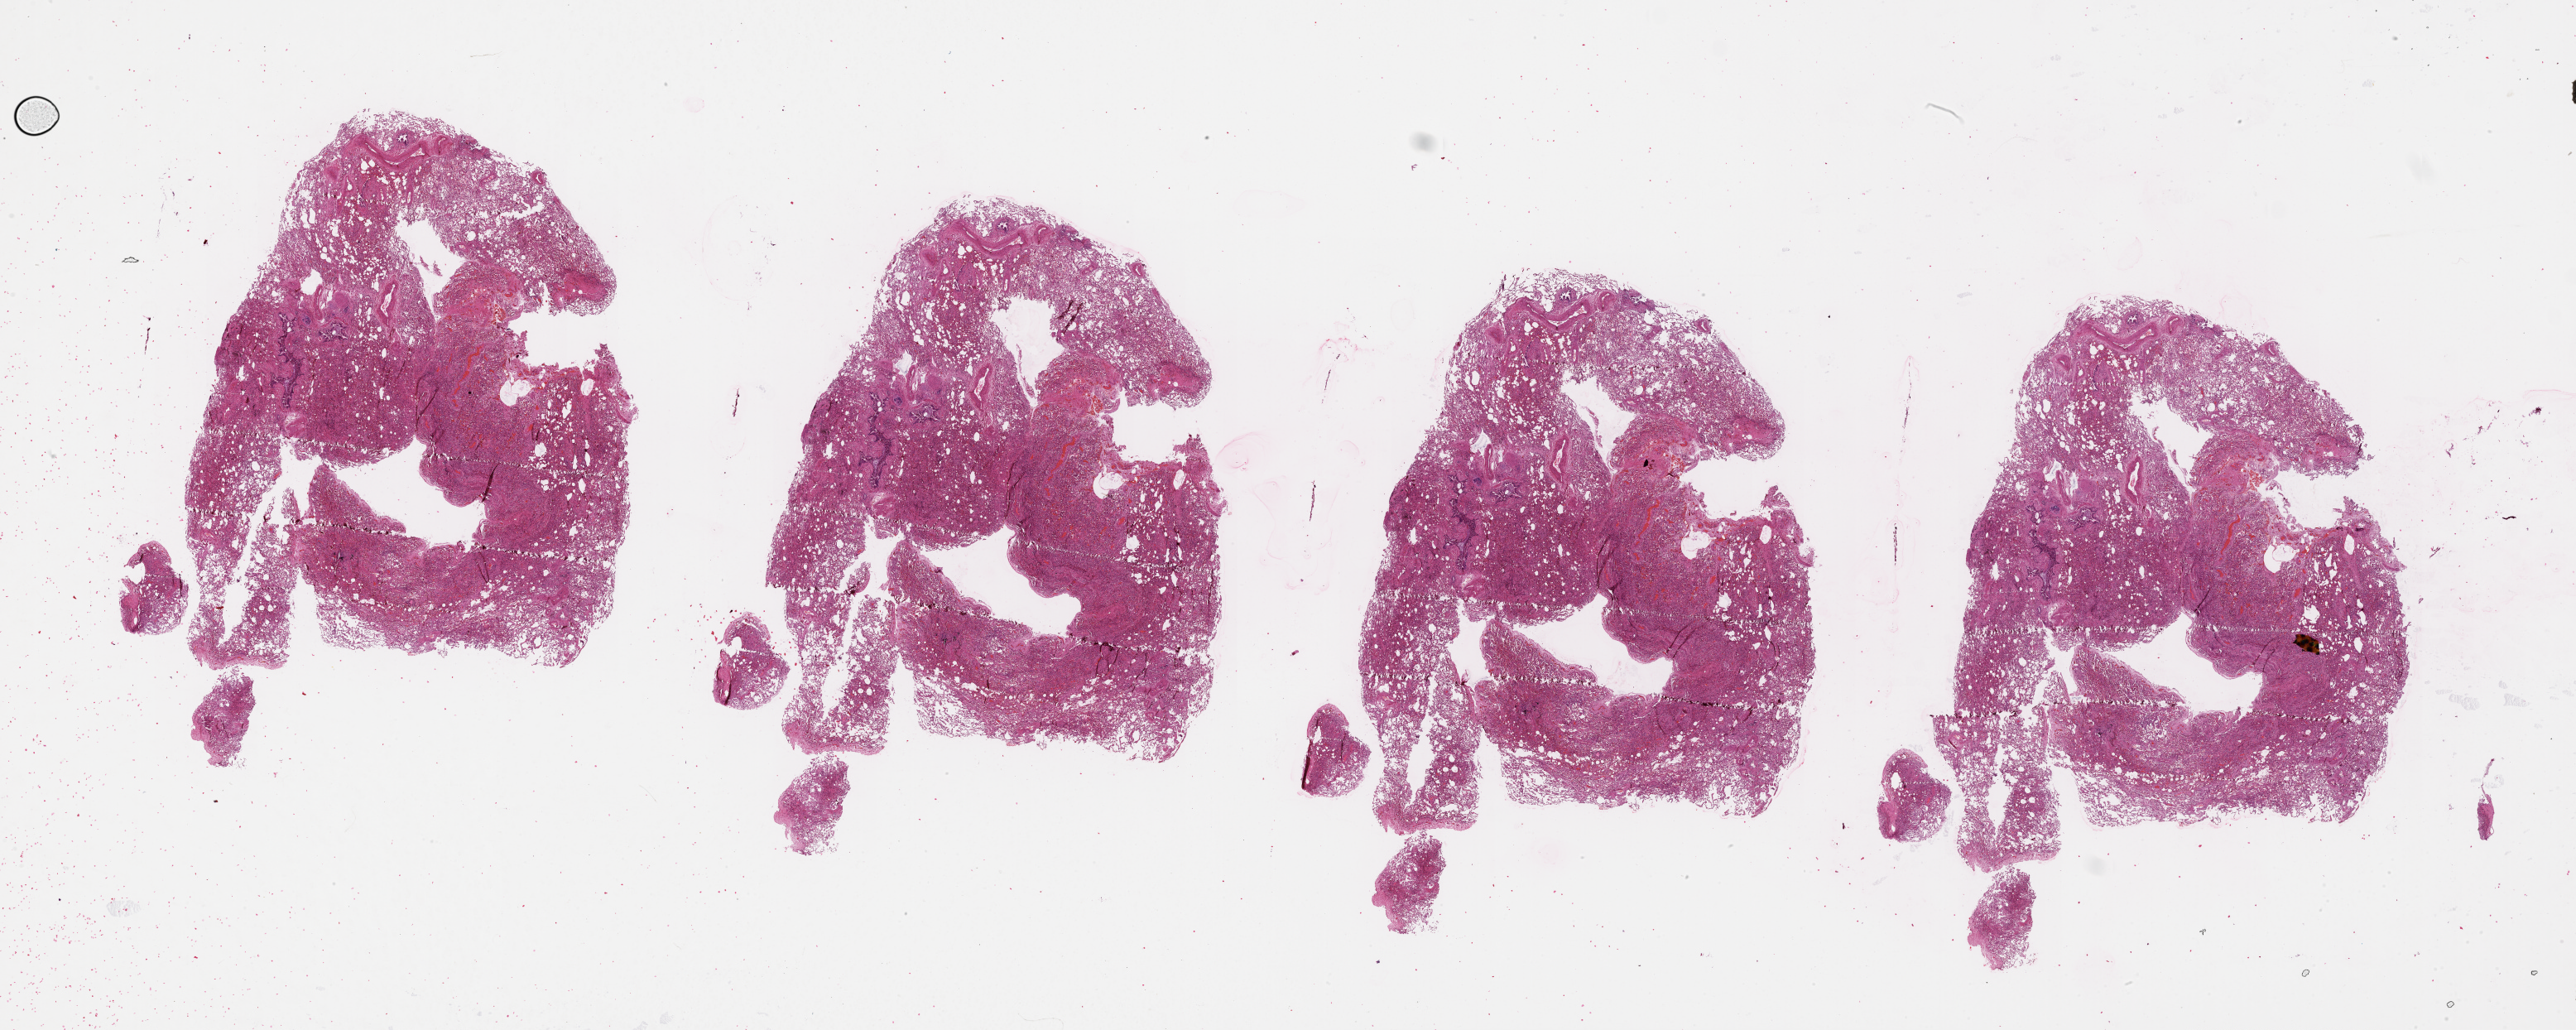
H&E whole-slide image, shown as a low-resolution overview of the whole scanned area (about 50.1 x 20.0 mm). Lung, tissue type not recorded.
• patient diagnosis (cohort enrolment): lung adenocarcinoma (lung)